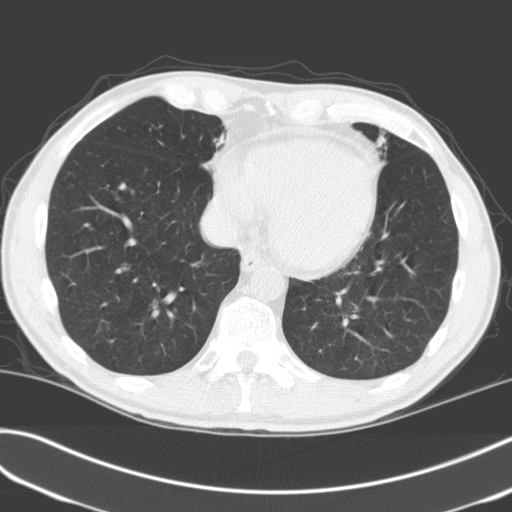
Low-dose screening chest CT, one axial slice. Slice 55 of 170 in the series (ordered by position). Lung window (W 1500 / L -600 HU). 3.2 mm slice thickness. 512 × 512 image matrix, field of view 351 × 351 mm.
Annotated regions visible in this slice (outlined manually by an expert reader):
- lesion 1 (tumor, upper lobe of left lung): bounding box <377,136,386,147> (left, top, right, bottom; pixels)